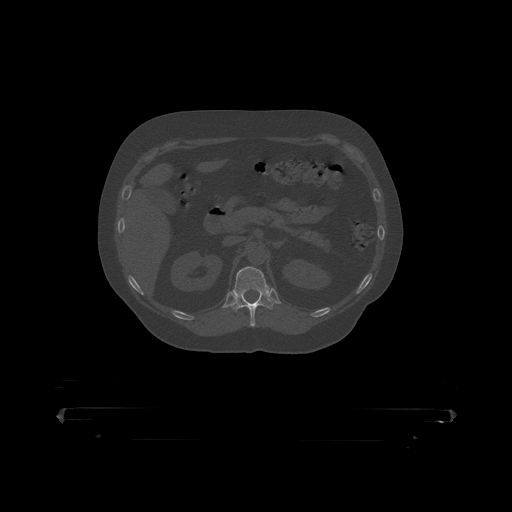
CT including the spine, one axial slice; position 173 of 390 along the scan axis; 120 kVp; bone window (W 1800 / L 400 HU); 512 × 512 image matrix. Male patient, age 60 years. Case-level facts recorded for this patient, not image findings: primary cancer: prostate.
Annotated regions visible in this slice (semi-automatic segmentation, software-assisted and operator-edited):
- T12 vertebra: bounding box [x1, y1, x2, y2] px = [230, 267, 275, 319]